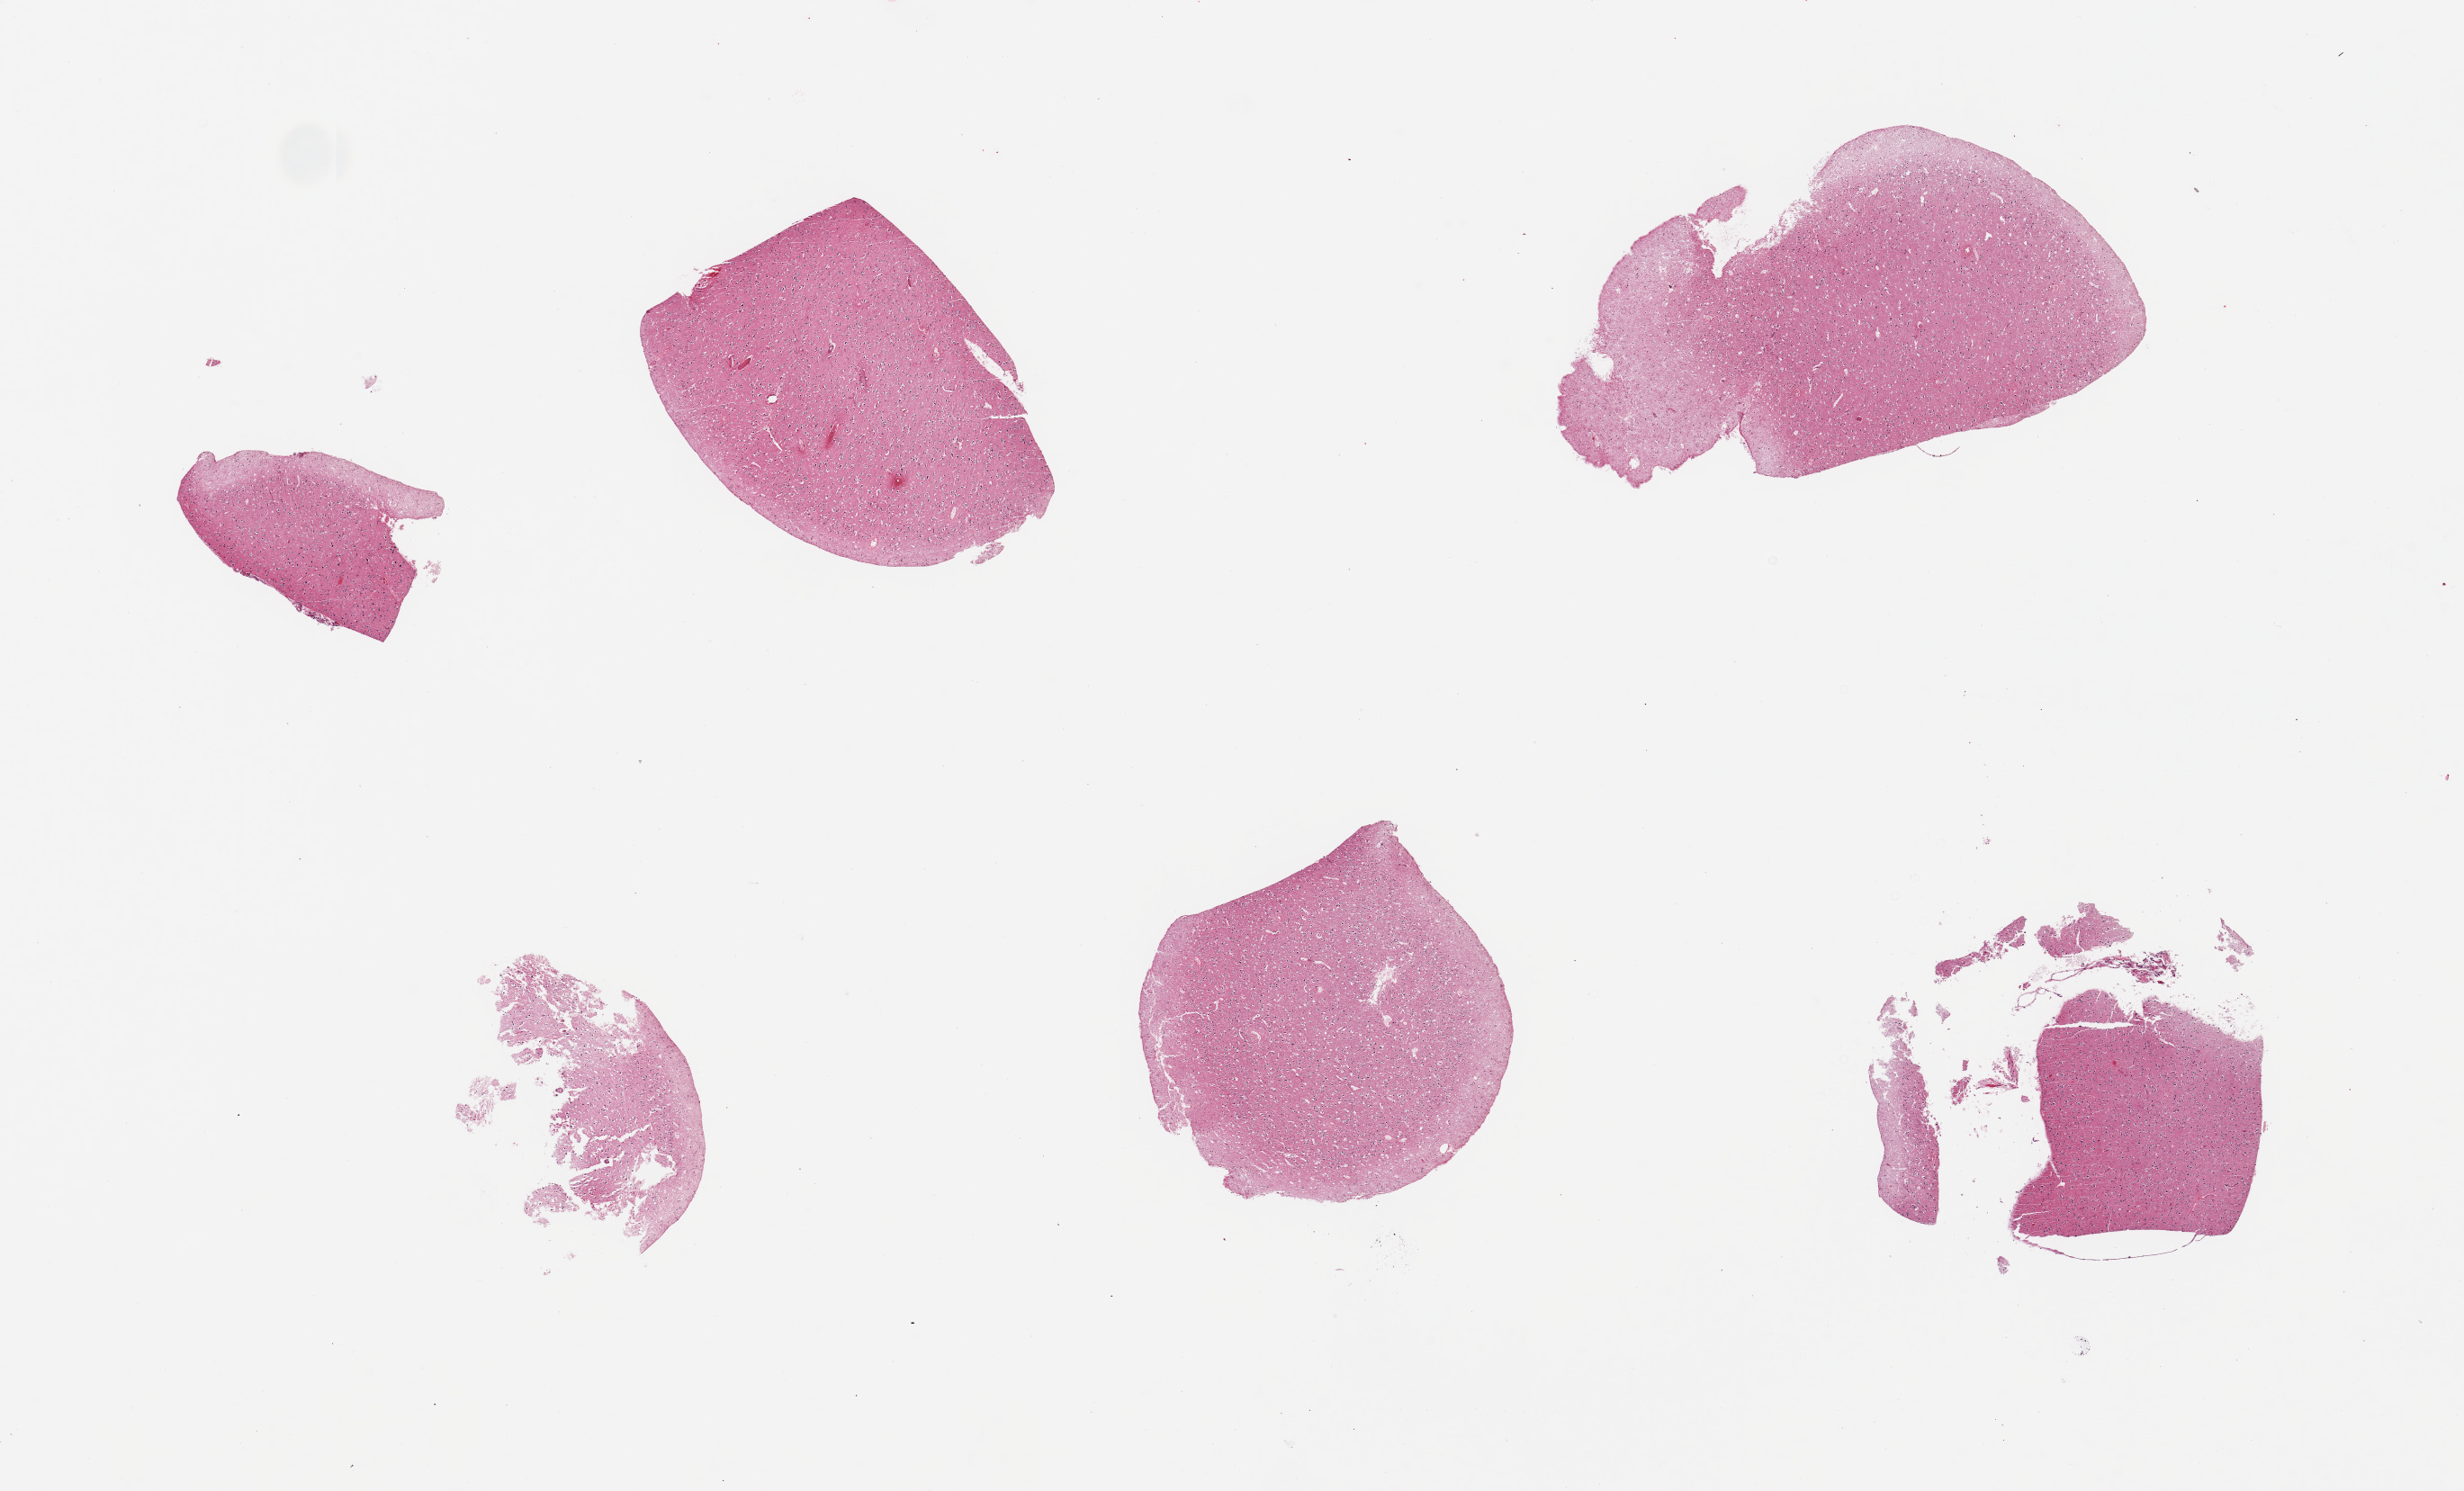
Whole-slide image, hematoxylin and eosin (H&E) stain, brightfield, a low-resolution overview of the entire scanned area, about 21.7 x 13.1 mm, PAXgene-fixed, paraffin-embedded tissue, sampled site (target tissue): cerebral cortex, tissue donor sample. Female donor.
Pathologist's review note for this sample: 6 fragmented pieces.